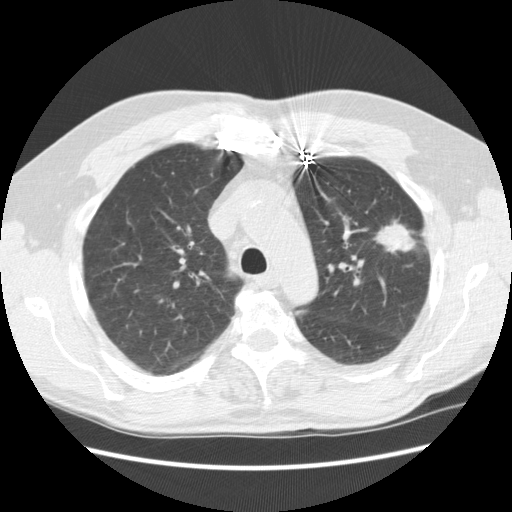
Low-dose screening chest CT, one axial slice. Position 175 of 231 along the scan axis. Reconstruction kernel STANDARD. 120 kVp. Lung window (W 1500 / L -600 HU). 2.5 mm slice thickness. 512 × 512 image matrix, field of view 362 × 362 mm.
Structures marked on this image (manually delineated by an expert):
- lesion 1 (tumor, upper lobe of left lung): bounding box [x1, y1, x2, y2] px = [374, 219, 416, 252]